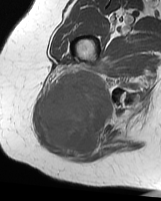
MRI of an extremity soft-tissue mass, one axial slice; position 39 of 70 along the scan axis; MR volume resampled by the dataset authors to the PET/CT grid (not the native acquisition matrix); 3.27 mm slice thickness; 161 × 201 image matrix. Female patient. Case-level facts recorded for this patient, not image findings: histological type: synovial sarcoma; grade: intermediate; site of the primary tumour: right buttock.
Annotated regions visible in this slice (expert contour drawn on MRI and transferred to this co-registered scan by the dataset authors):
- gross tumour volume including surrounding oedema: bounding box [x1, y1, x2, y2] px = [40, 68, 114, 158]
- gross tumour volume (mass): [40, 68, 114, 155]